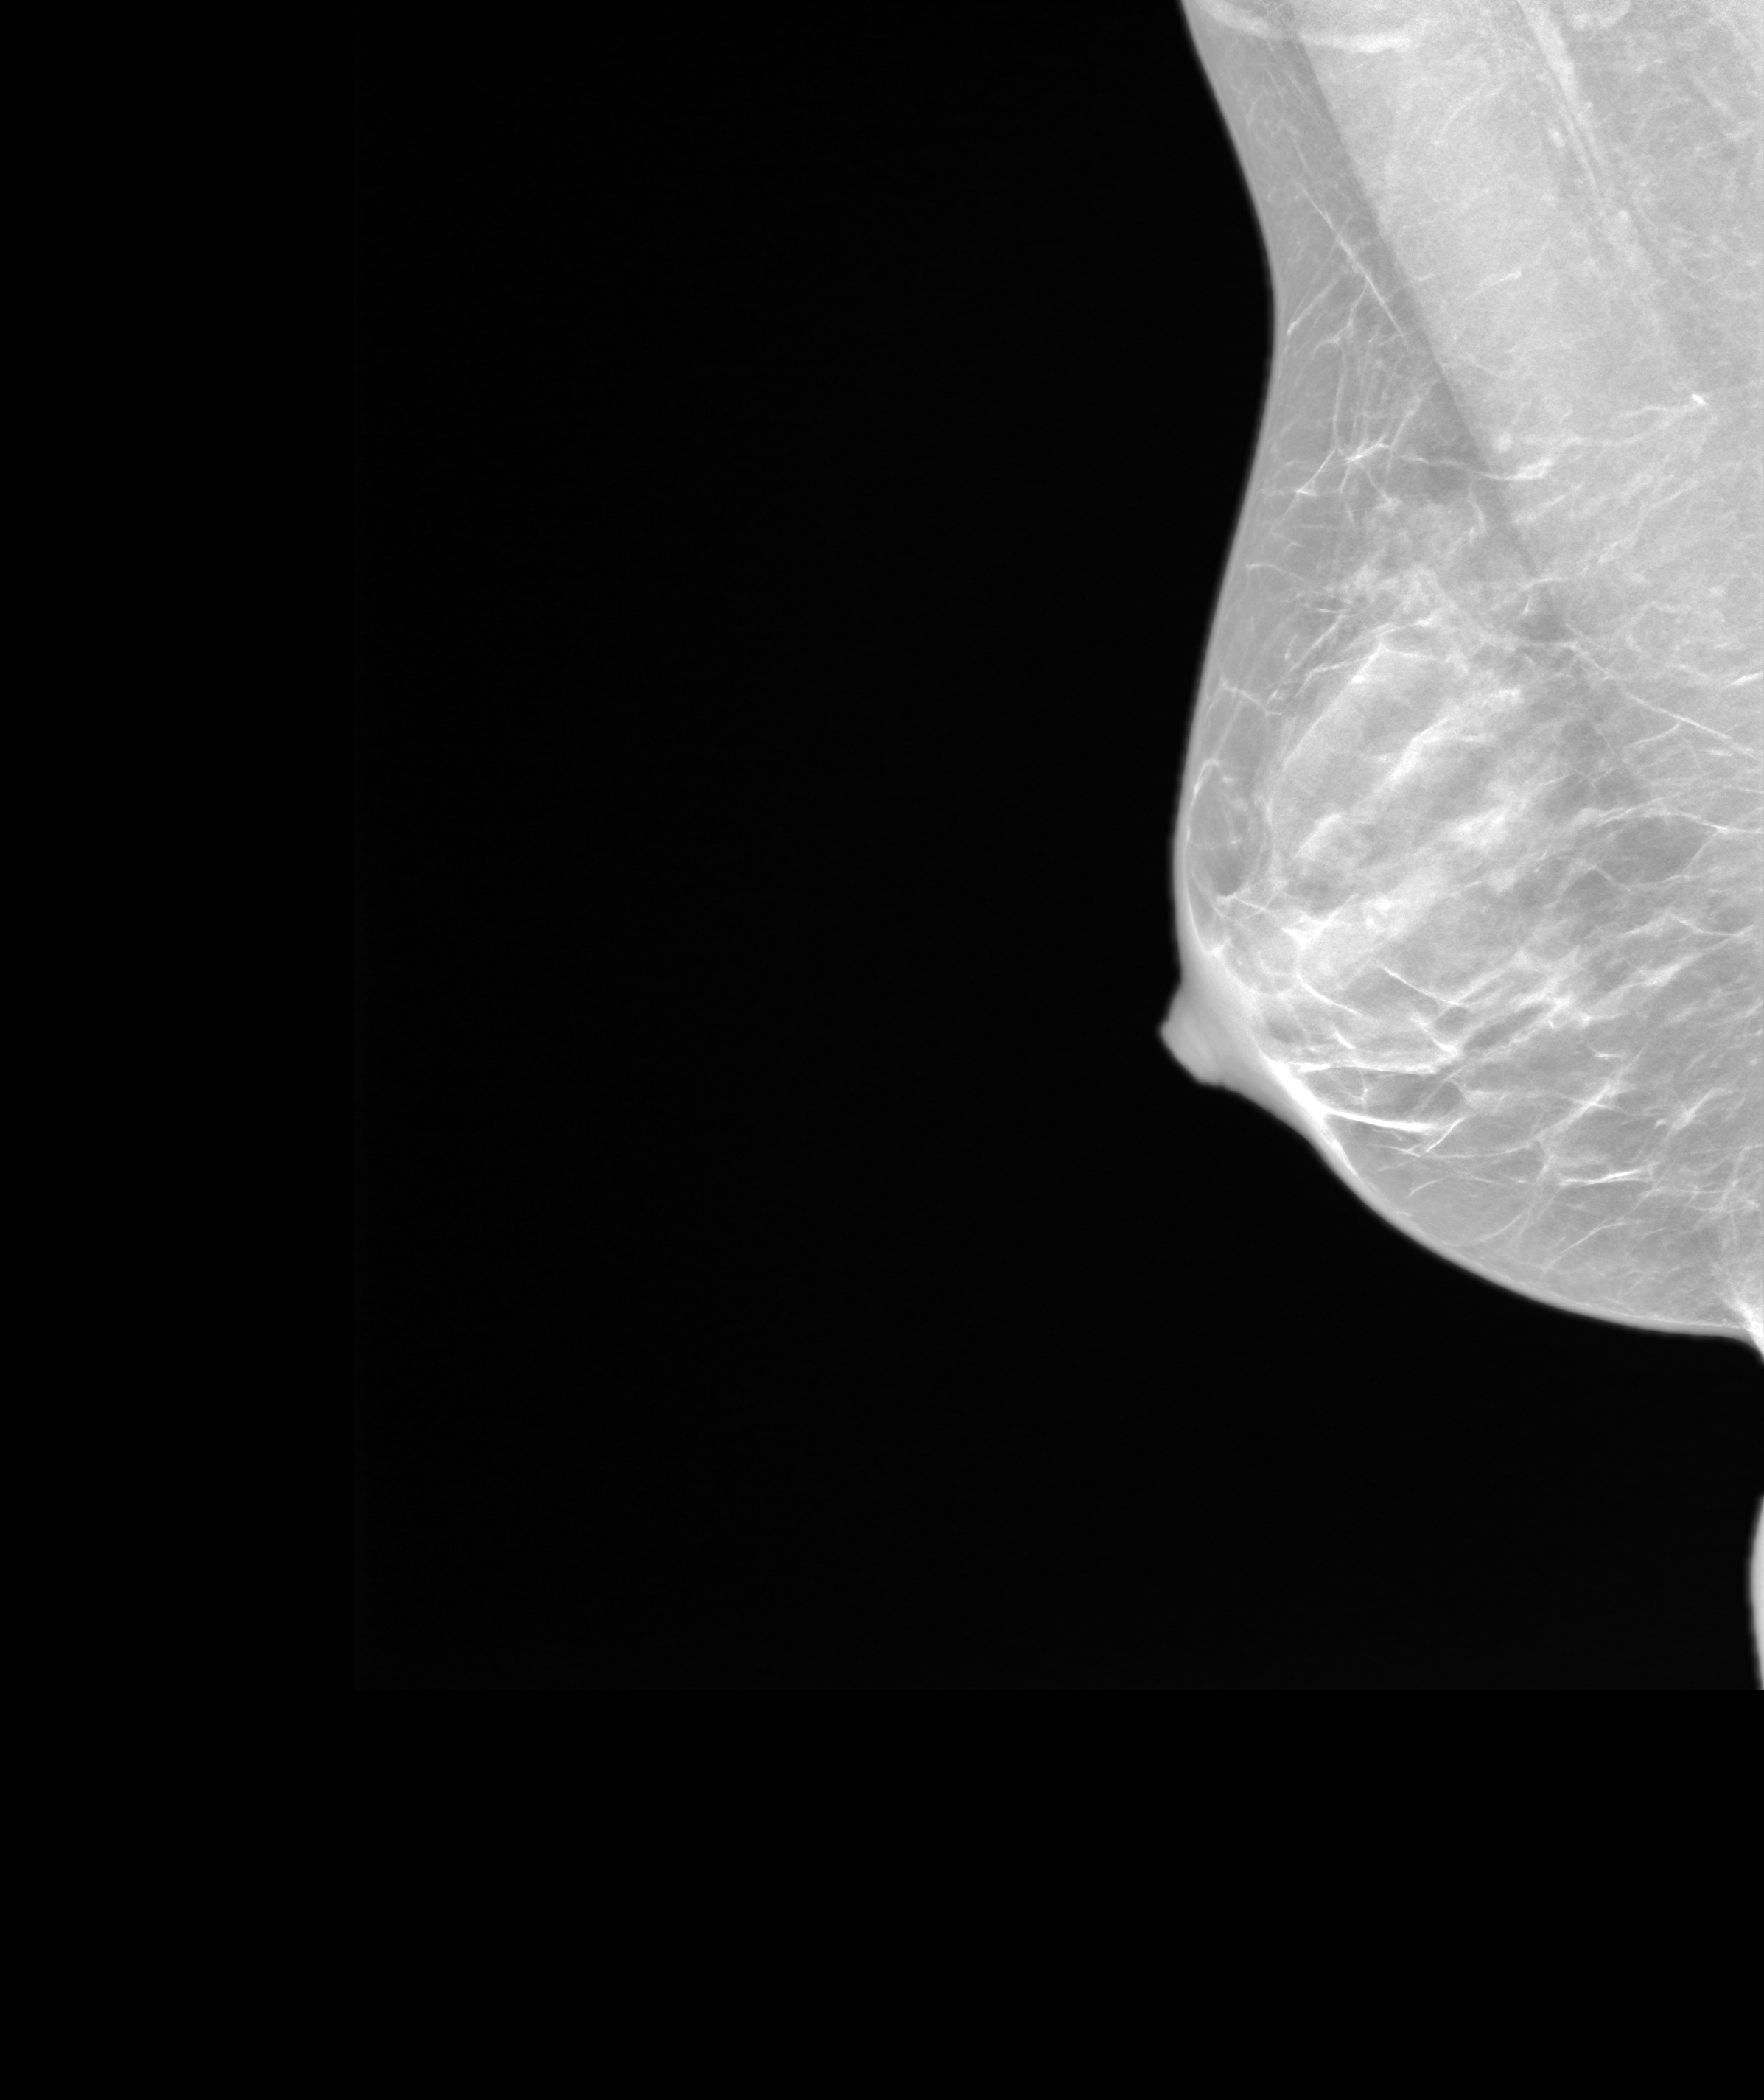
Synthesized 2-D mammogram reconstructed from digital breast tomosynthesis; right breast; MLO view; screening examination. Patient aged 48 years (female).
Breast density at the screening exam (both breasts): heterogeneously dense (BI-RADS density category c). Final BI-RADS assessment for this screening round (tomosynthesis exam, both breasts): category 2. Recall: no recall after this screen.